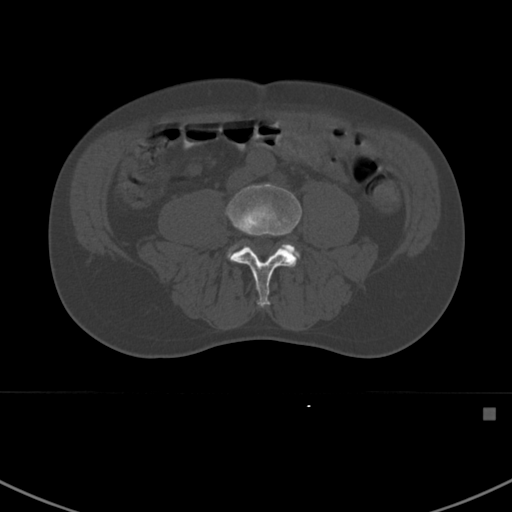
CT including the spine, one axial slice; position 236 of 412 along the scan axis; reconstruction kernel Br40s; bone window (W 1800 / L 400 HU); 512 × 512 image matrix. Patient: male, 59 years. From the clinical record (not read from this slice): primary cancer: prostate.
Outlined on this slice (semi-automatically segmented with operator editing):
- L4 vertebra: bounding box <226,184,302,307> (left, top, right, bottom; pixels)
- L5 vertebra: <226,244,300,260>